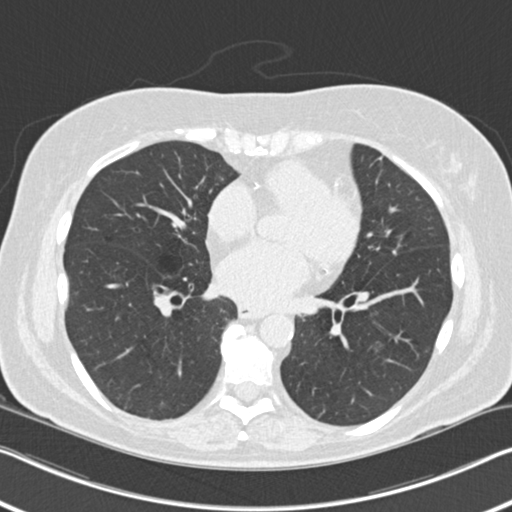
Chest CT (low-dose screening protocol), one axial image; second annual screen; lung window (W 1500 / L -600 HU); 2 mm slice thickness; 120 kVp; slice 114 of 202 in the series; 512 × 512 image matrix. Female, age 60 years at enrolment. Current smoker at enrolment.
Expert-annotated lung lesion, box from (x=377, y=234) to (x=408, y=265) px. The screening reader recorded 6 non-calcified nodules or masses ≥4 mm on this exam (right upper lobe, right middle lobe, right lower lobe, right lower lobe, left lower lobe, lingula); which of them this box marks is not recorded. Official screen result: positive, change unspecified: nodule(s) >= 4 mm or enlarging nodule(s), mass(es), or other non-specific abnormalities suspicious for lung cancer. Lung cancer was diagnosed 495 days after this screen: non-small cell carcinoma, left upper lobe, poorly differentiated (G3), stage IB (AJCC 6th edition), 7 mm at pathology.